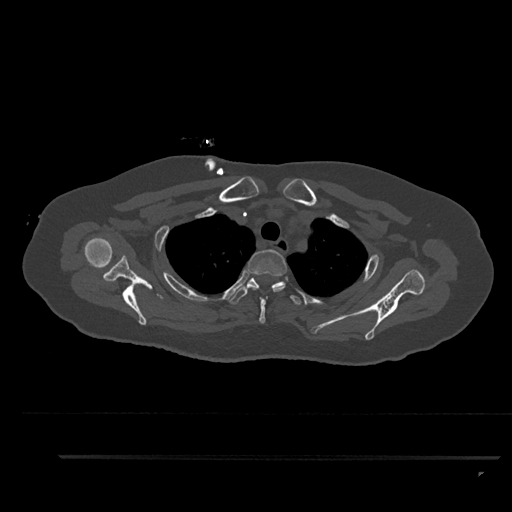
CT including the spine, one axial slice. Position 704 of 797 along the scan axis. Reconstruction kernel Br40s/3. 120 kVp. Bone window (W 1800 / L 400 HU). 512 × 512 image matrix, field of view 408 × 408 mm. Female patient, age 44 years. Case-level facts recorded for this patient, not image findings: primary cancer: renal.
Structures marked on this image (semi-automatic segmentation, software-assisted and operator-edited):
- T1 vertebra: bounding box <282,284,285,286> (left, top, right, bottom; pixels)
- T2 vertebra: <247,249,287,324>
- T3 vertebra: <229,274,302,305>